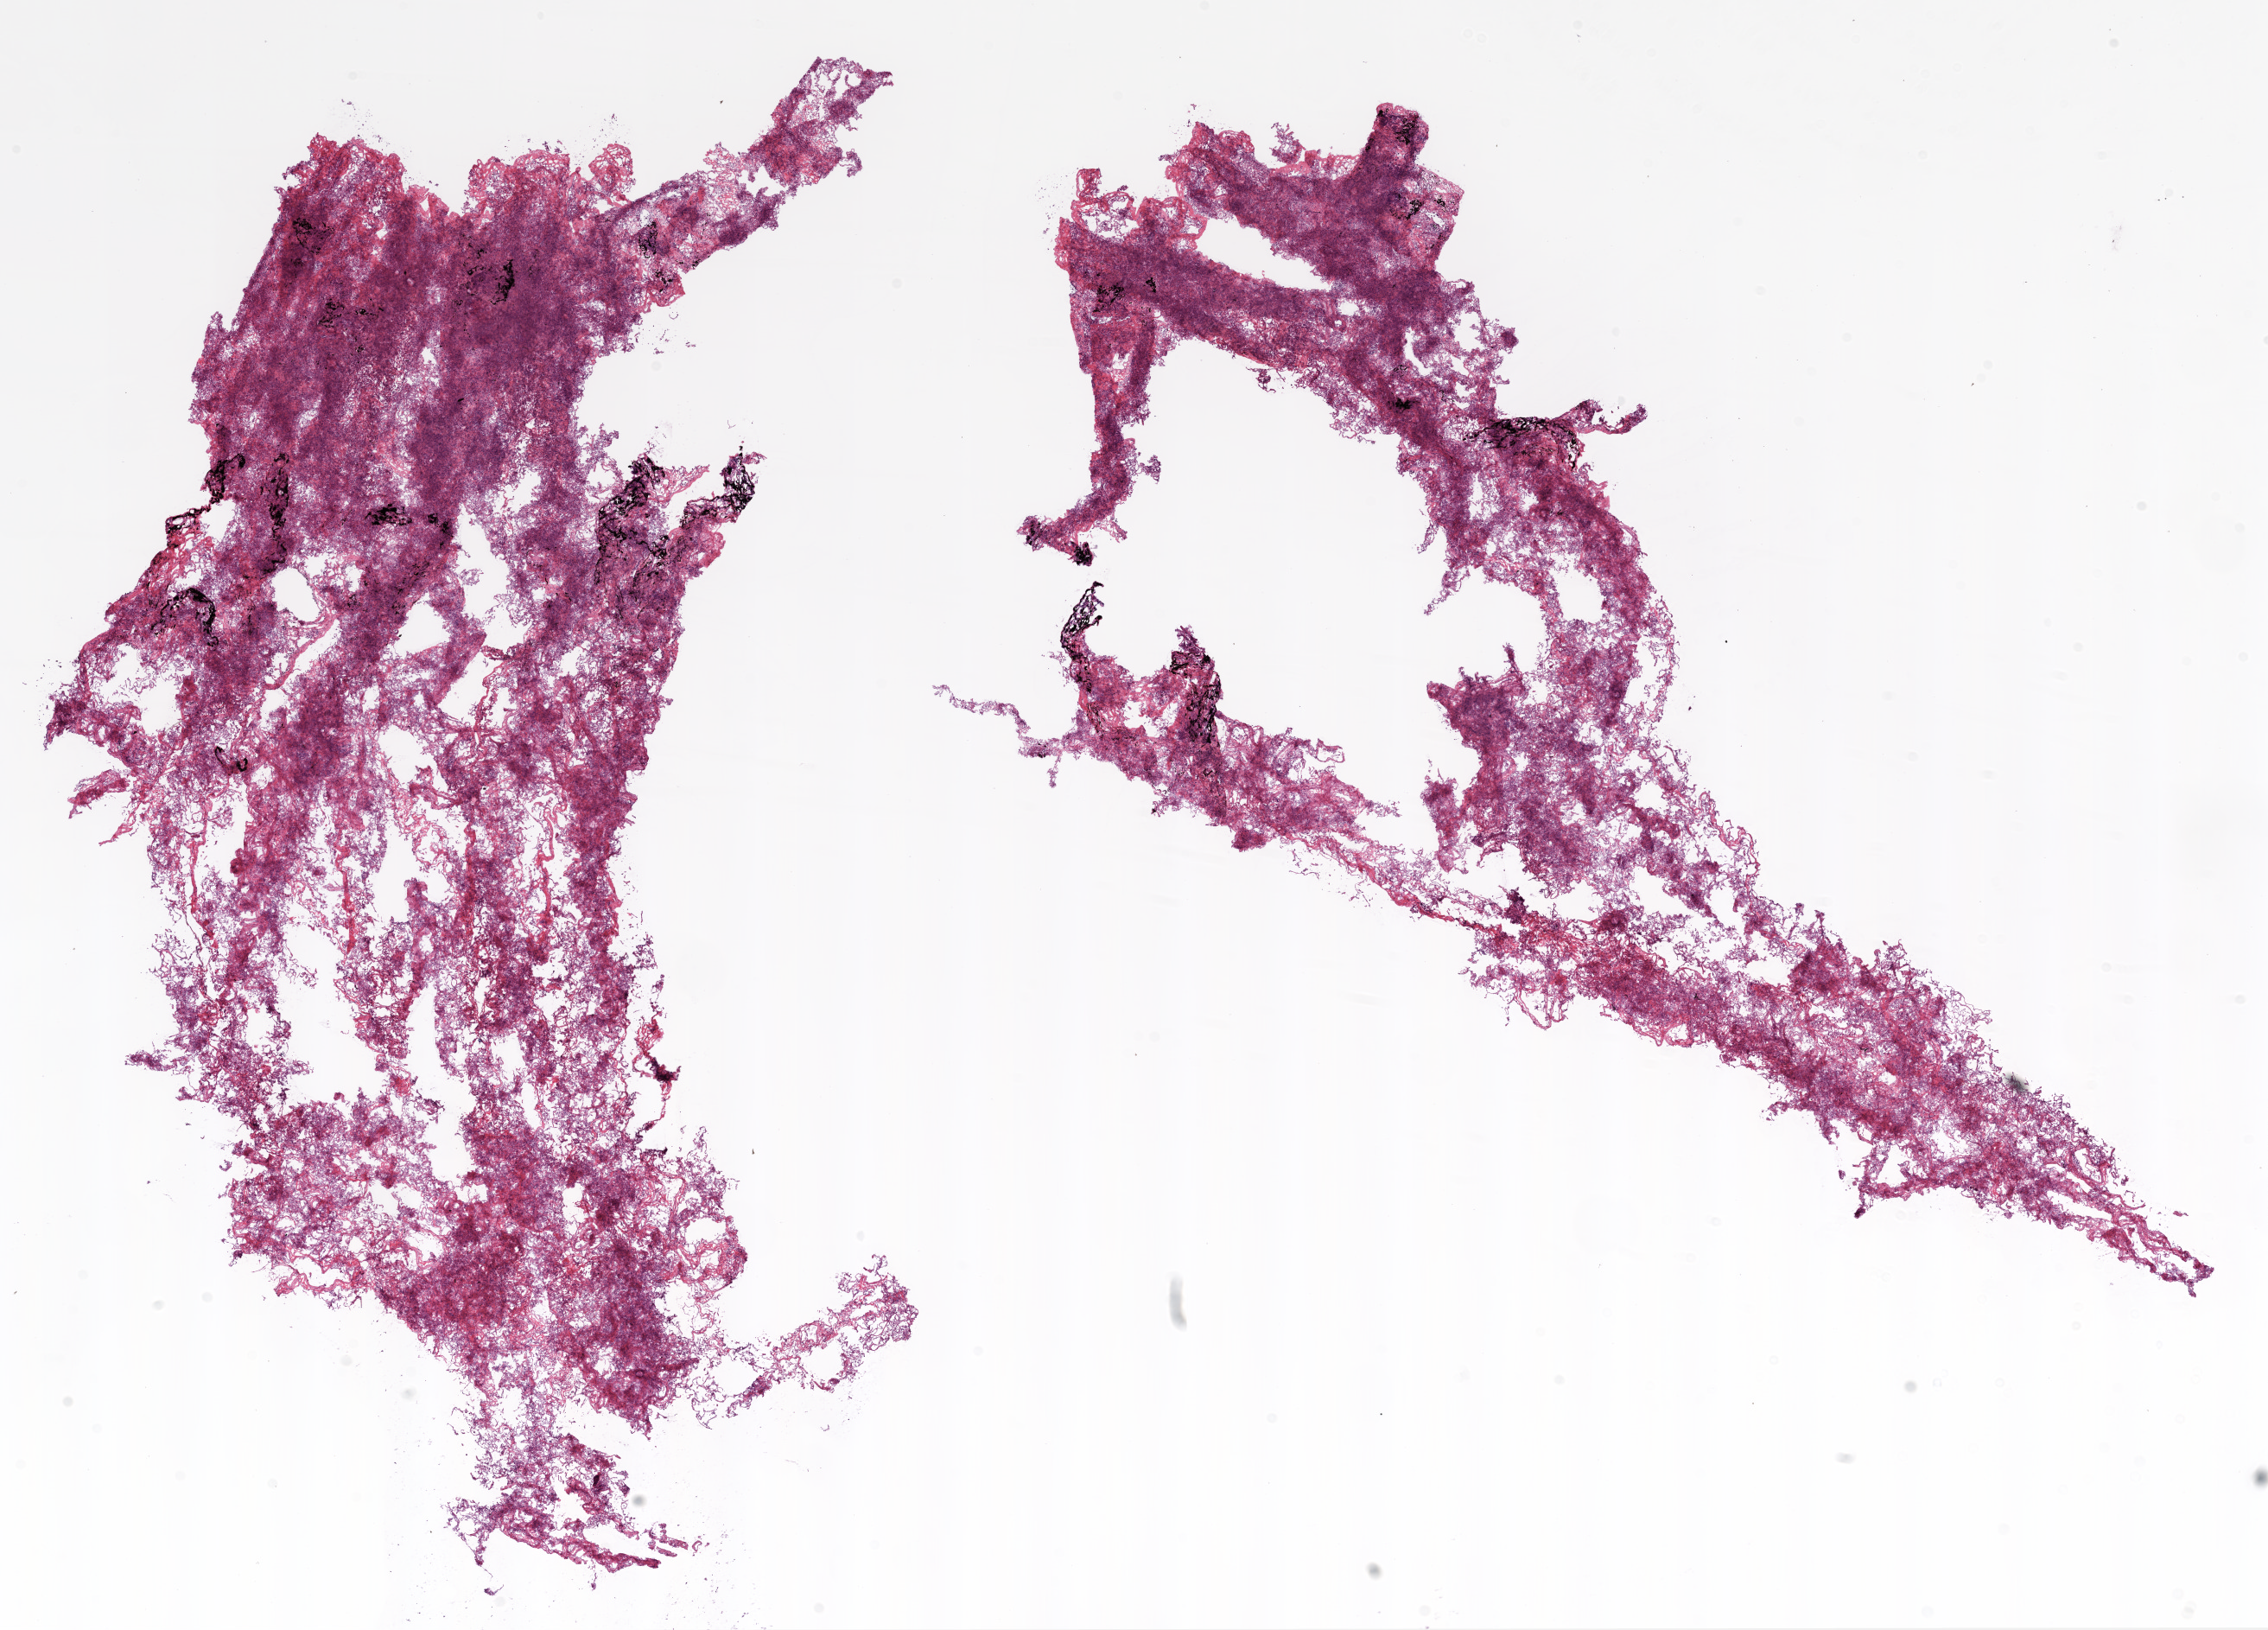
H&E-stained whole-slide image, shown as a low-resolution overview of the whole scanned area (about 21.1 x 15.1 mm, from a 20x scan). Frozen section from the bottom of the tissue portion. Lung, solid tissue normal (non-tumour tissue) sample. Male patient; age at initial diagnosis 81 years.
- this section: solid tissue normal (non-tumour) sample from the same patient
- patient diagnosis: Squamous cell carcinoma, NOS (lower lobe, lung)